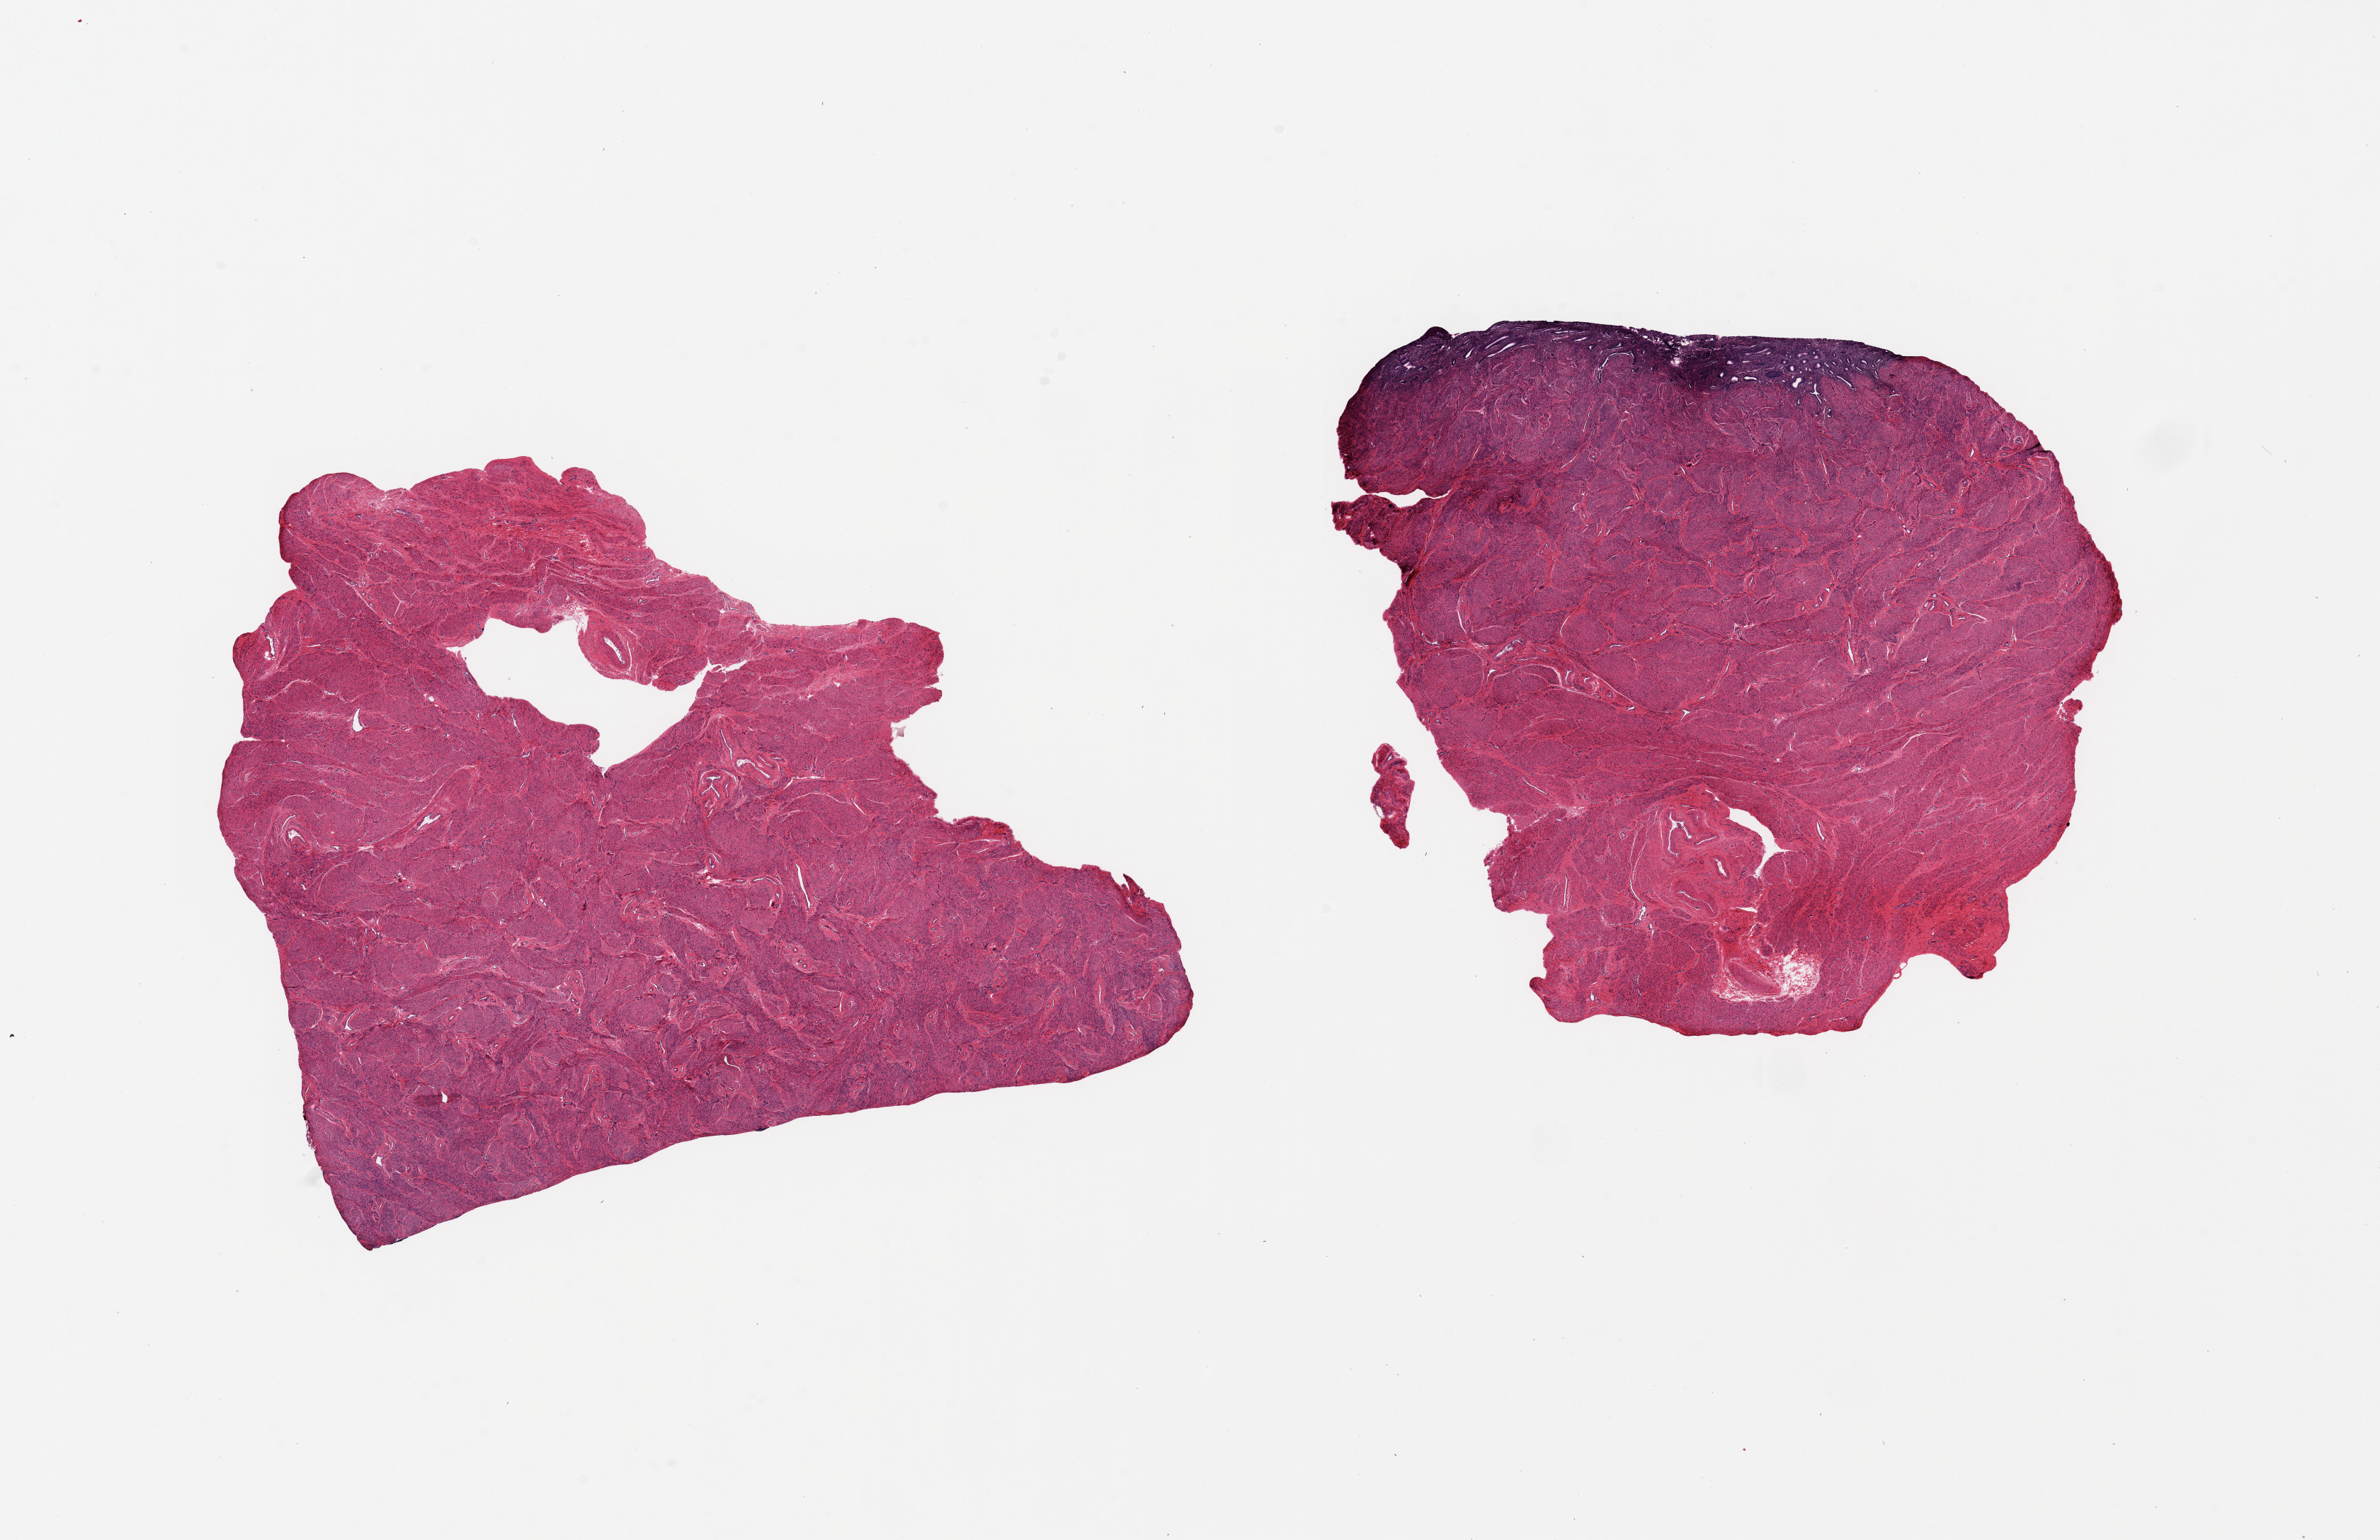
Digitized hematoxylin and eosin (H&E)-stained section, a low-resolution overview of the entire scanned area, about 26.6 x 17.2 mm (slide scanned at 20x). PAXgene-fixed paraffin-embedded (PFPE) section. Target tissue: uterus. Donor tissue sample. Donor sex: female.
Reviewer comment on this tissue sample: 2 pieces, 10x8 & 8.5x8mm; one has thin endometrium, other has no endometrium on this cut.